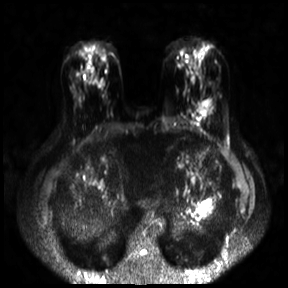
Breast MRI, one axial slice. Slice 11 of 30 in the series (ordered by position). Diffusion-weighted series; image 2 of 4 stored at this slice position (different b-values; order by instance number). 3 T. 288 × 288 image matrix, field of view 360 × 360 mm. Female patient.
Annotated regions visible in this slice (outlined manually by an expert reader):
- tumour on diffusion-weighted imaging: bounding box <198,99,213,112> (left, top, right, bottom; pixels)